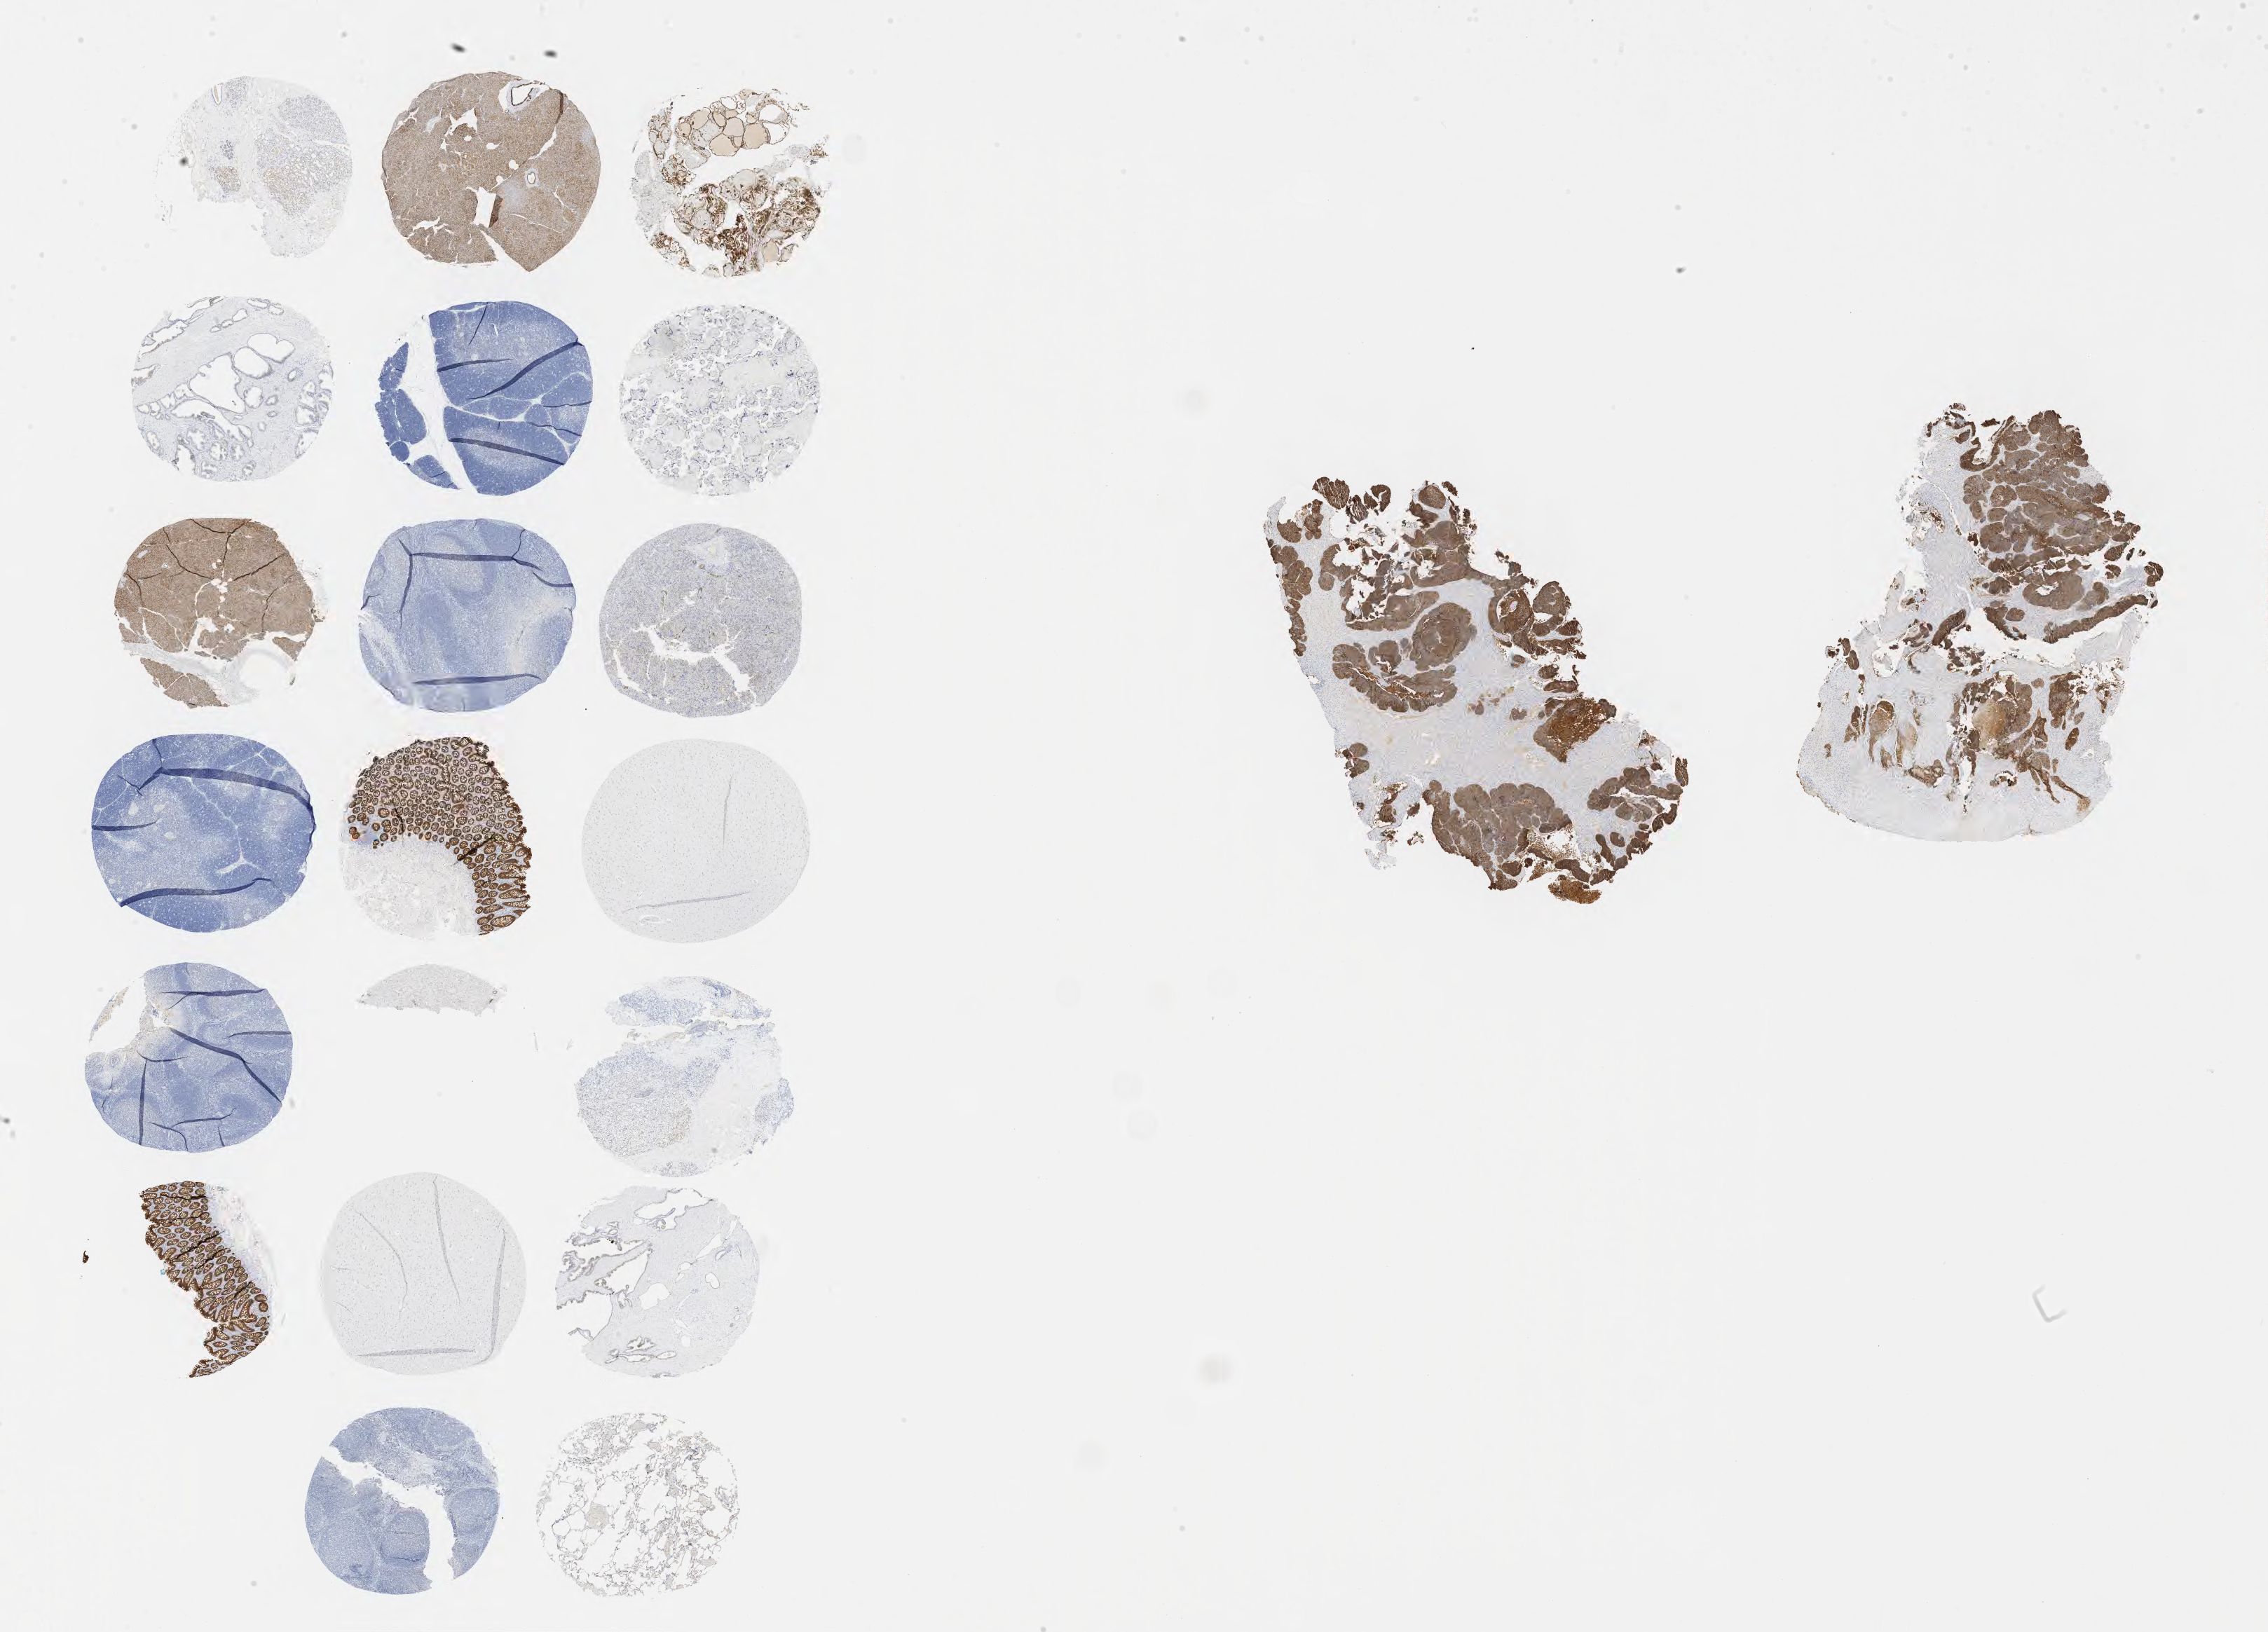
Immunohistochemistry (IHC) whole-slide image stained for Ber-EP4 — shown as a low-resolution overview of the whole scanned area (about 26.2 x 18.8 mm). Tumor tissue. Site: cervix. Female patient, age 38 years.
Diagnosis: Squamous cell carcinoma, large cell, nonkeratinizing, NOS.